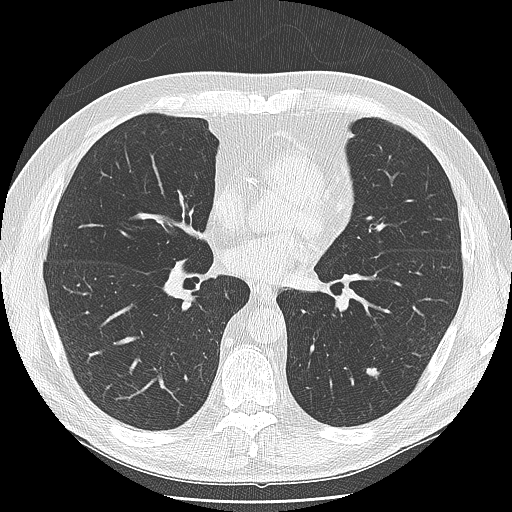
Low-dose screening chest CT, one axial slice; slice 80 of 166 in the series (ordered by position); reconstruction kernel LUNG; lung window (W 1500 / L -600 HU); 2.5 mm slice thickness; 512 × 512 image matrix, field of view 360 × 360 mm.
Annotated regions visible in this slice (manually delineated by an expert):
- lesion 1 (tumor, lower lobe of left lung): bounding box <366,368,380,379> (left, top, right, bottom; pixels)